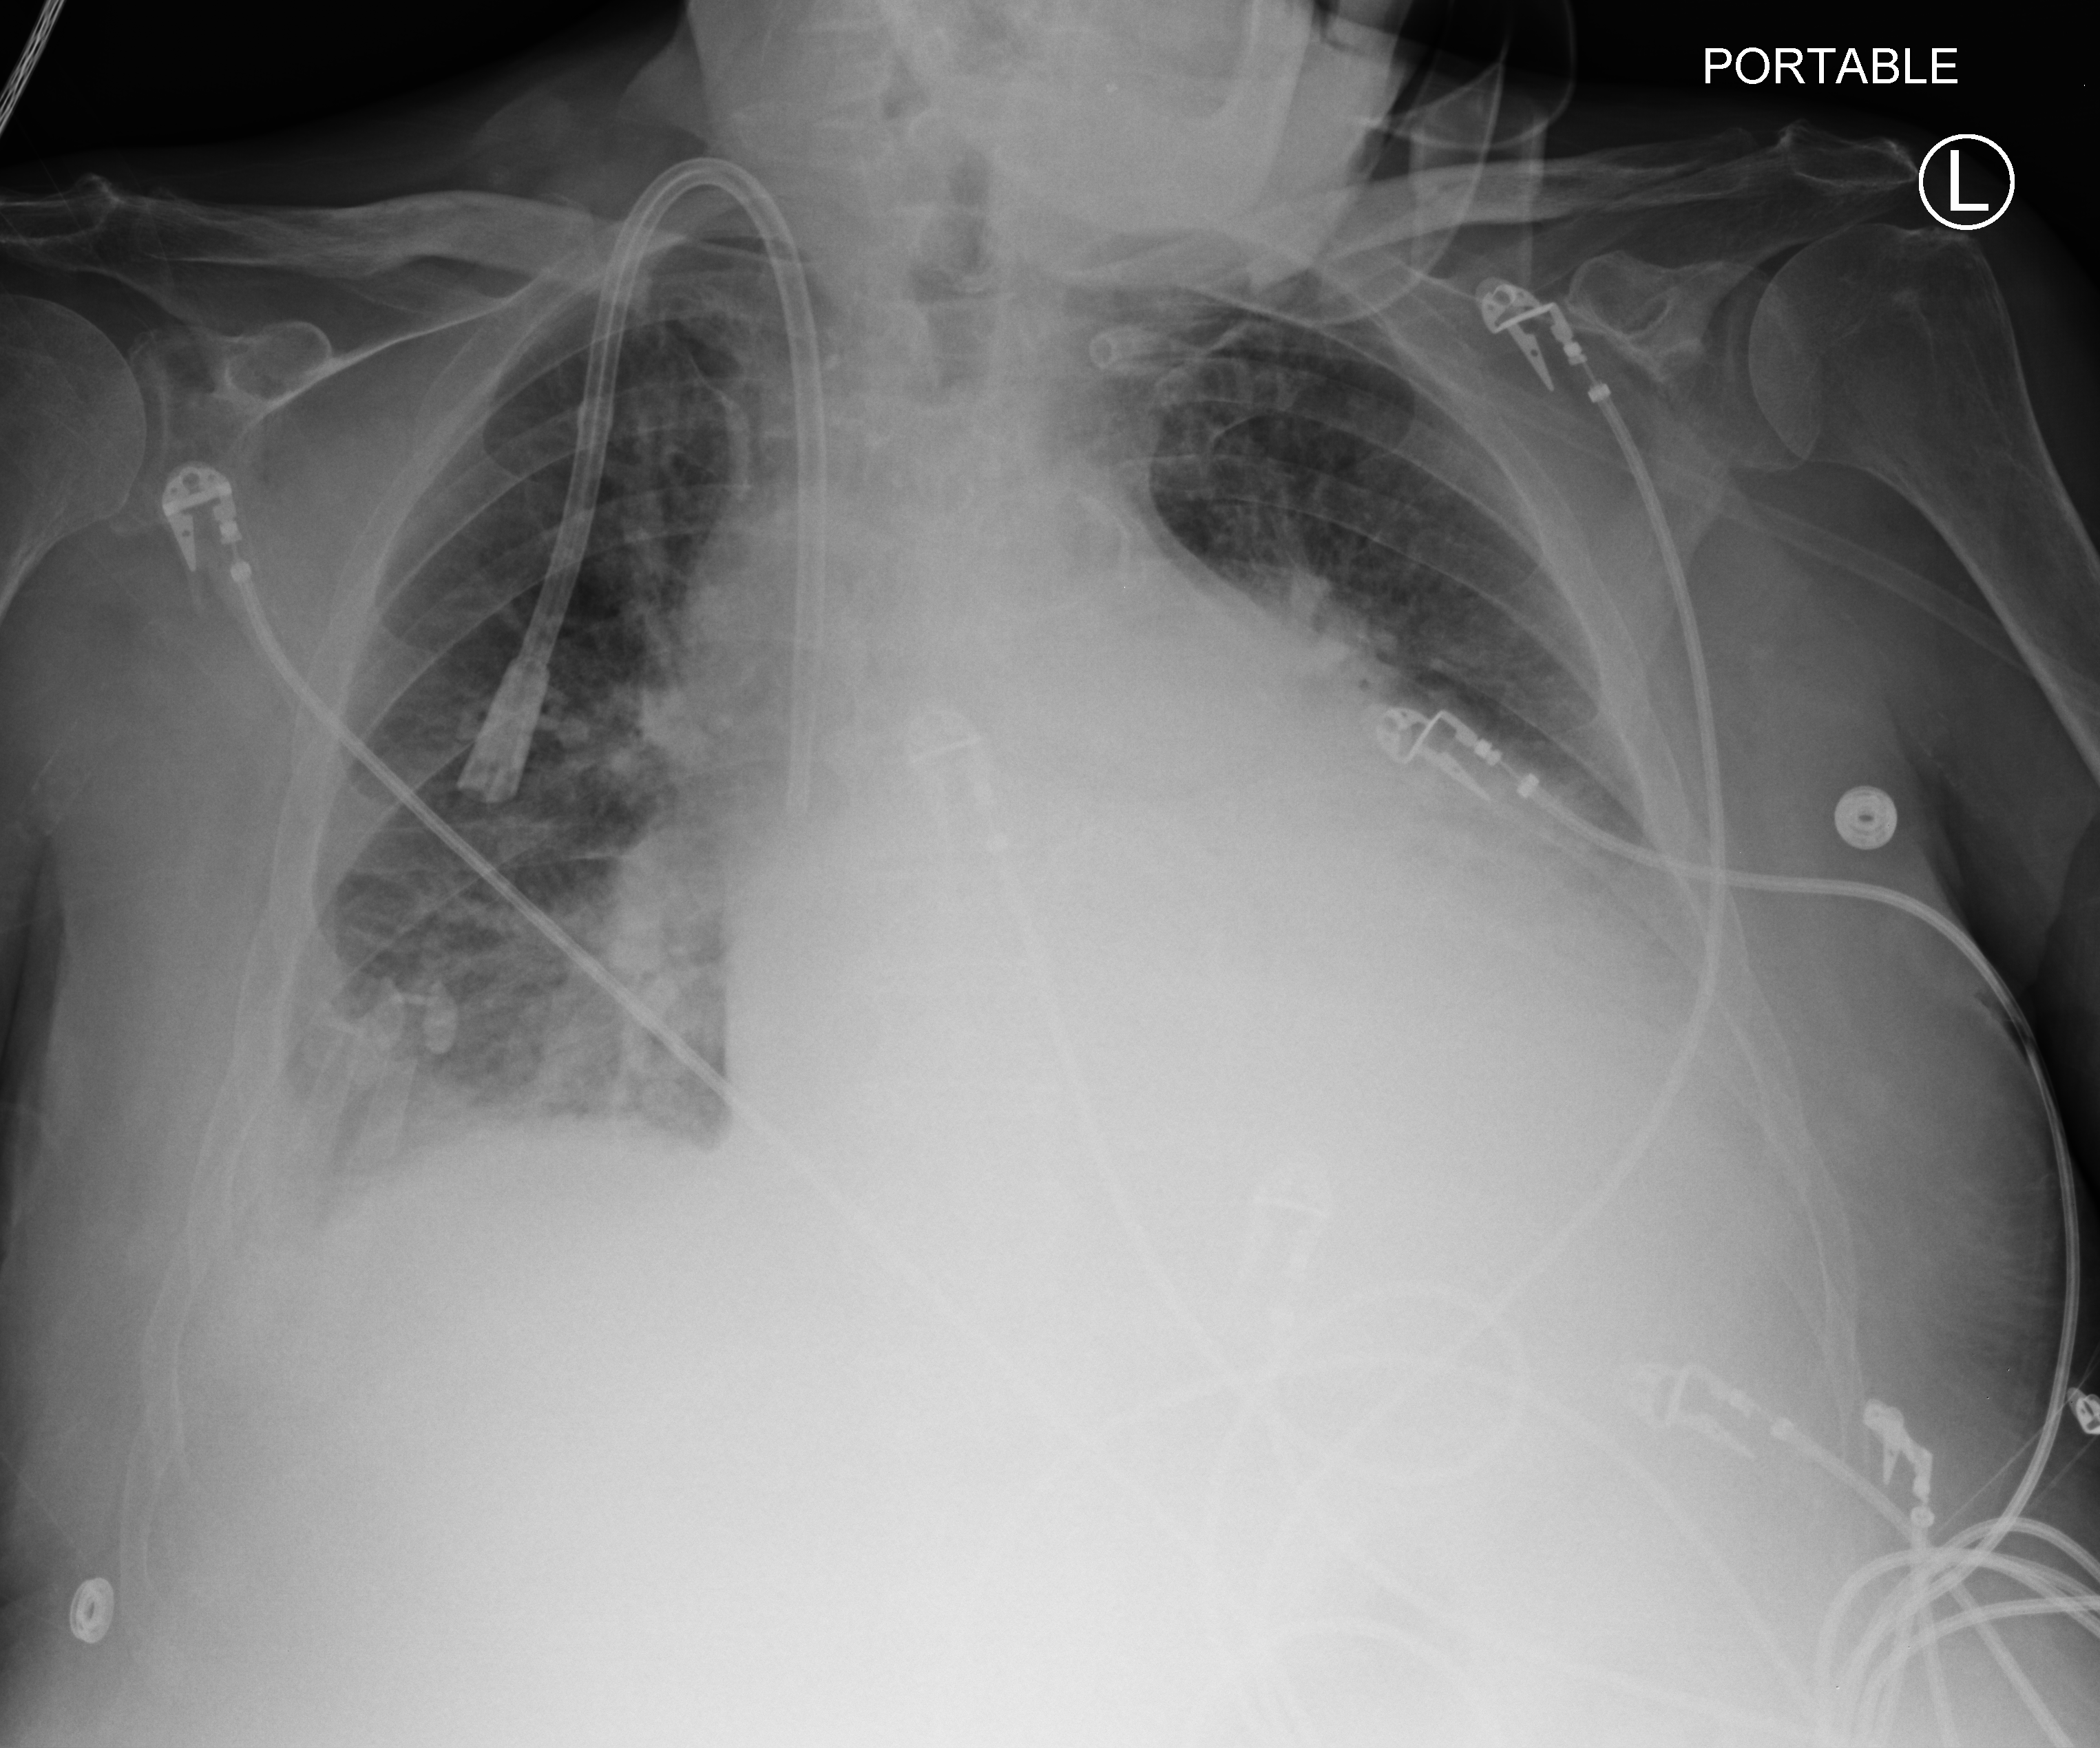
Portable chest radiograph, anteroposterior (AP) projection. Male patient hospitalised with COVID-19, age 60–74 years.
From the hospital-stay record, not from the radiograph (when in the stay this image was taken is not recorded): hypertension (admission record): yes.